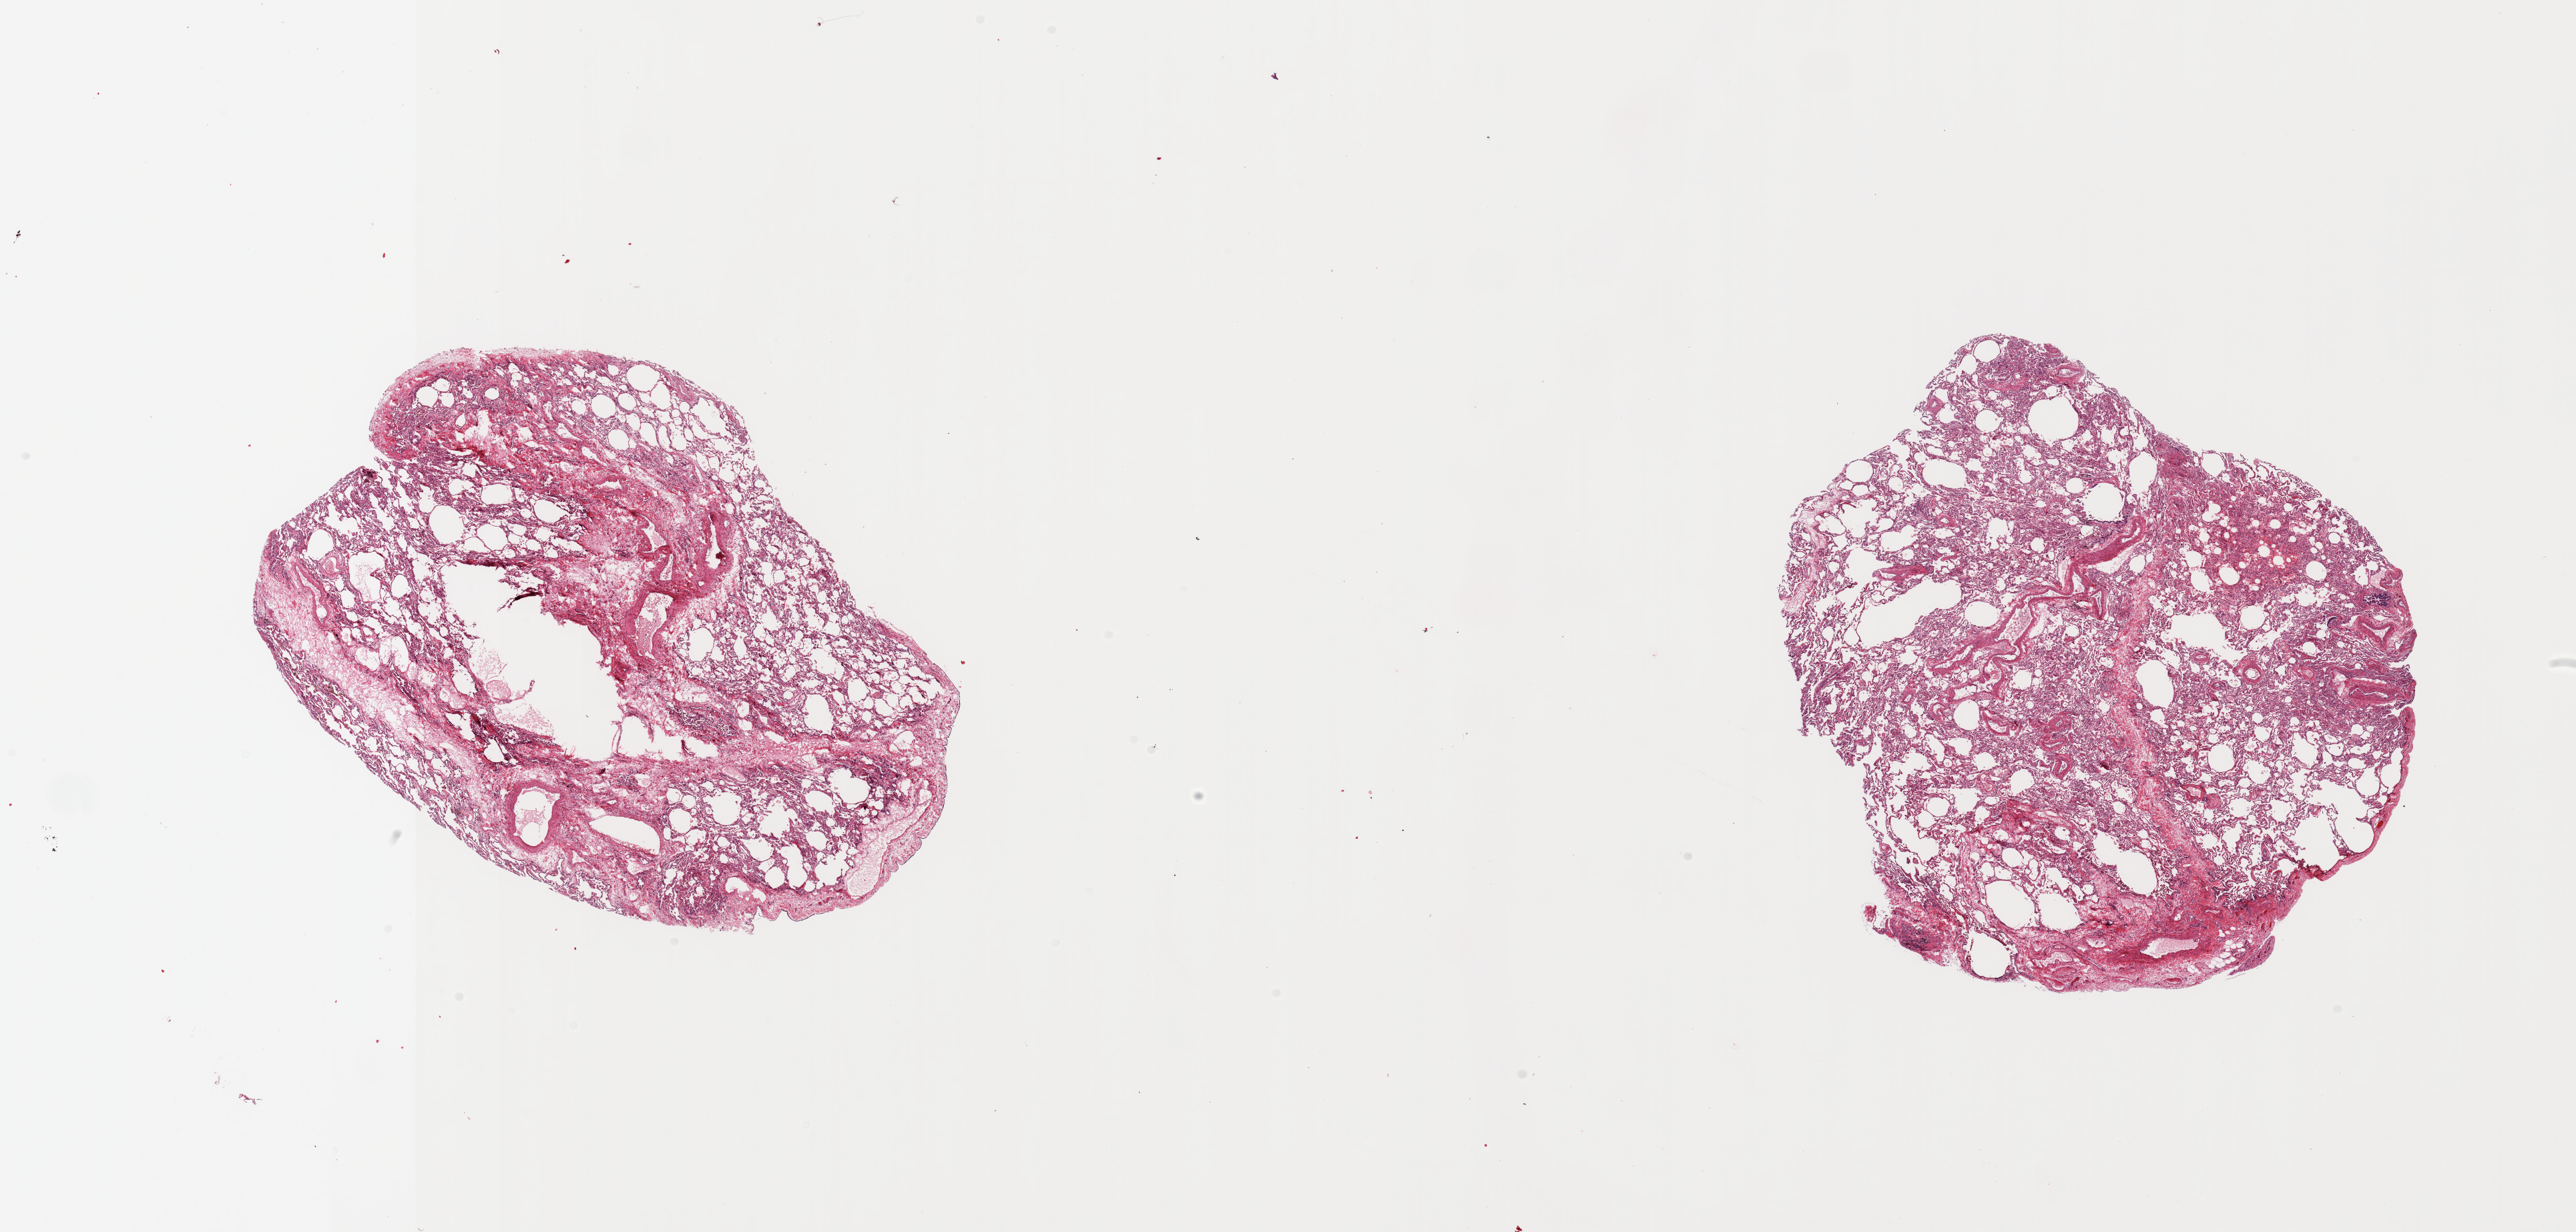
H&E whole-slide image — low-resolution overview of the scanned area, about 30.5 x 14.6 mm, PAXgene-fixed paraffin-embedded (PFPE) section, sampled site (target tissue): lung, tissue donor sample.
- review note (as recorded): 2 pieces; includes pleura (not target region), many pulmonary macrophages, some collapse/fibrosis/larger vessels present